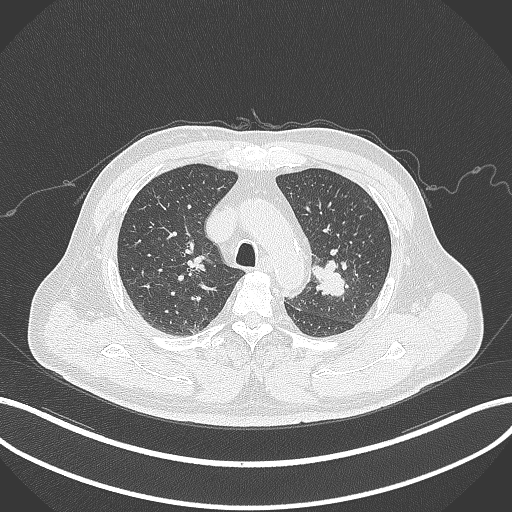
Chest CT, one axial slice. Slice 225 of 286 in the series (ordered by position). 120 kVp. Lung window (W 1500 / L -600 HU). 1 mm slice thickness. 512 × 512 image matrix, field of view 400 × 400 mm. Patient: male, 67 years. Case-level facts recorded for this patient, not image findings: clinical TNM (as recorded): T2a N1 M0; histopathological grade: G3.
Structures marked on this image (rectangle marked by the reading radiologist):
- lung tumour (recorded histology: adenocarcinoma): bounding box (x1, y1, x2, y2) in pixels: (309, 257, 348, 298)